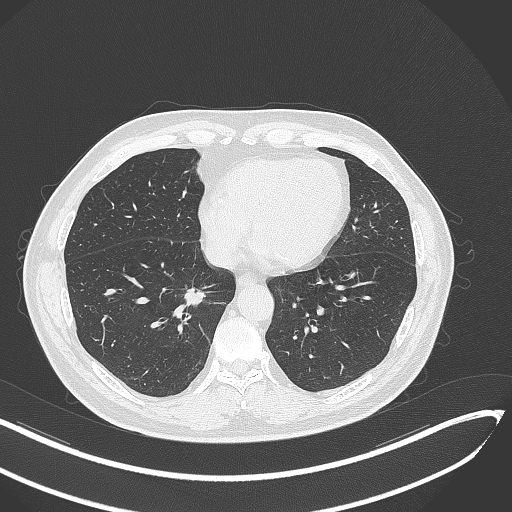
Chest CT, one axial slice. Position 131 of 429 along the scan axis. 120 kVp. Lung window (W 1500 / L -600 HU). 1 mm slice thickness. 512 × 512 image matrix, field of view 400 × 400 mm. Patient: male, 62 years. Case-level facts recorded for this patient, not image findings: clinical TNM (as recorded): T1b N0 M0; histopathological grade: G2.
Outlined on this slice (rectangle marked by the reading radiologist):
- lung tumour (recorded histology: adenocarcinoma): bounding box [x1, y1, x2, y2] px = [184, 286, 217, 308]